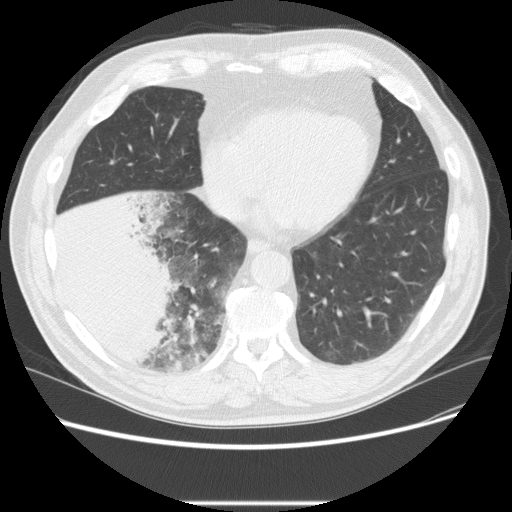
Low-dose screening chest CT, one axial slice. Position 73 of 233 along the scan axis. Reconstruction kernel STANDARD. Lung window (W 1500 / L -600 HU). 512 × 512 image matrix, field of view 380 × 380 mm.
Structures marked on this image (manually delineated by an expert):
- lesion 3 (tumor, lower lobe of right lung): bounding box (x1, y1, x2, y2) in pixels: (52, 192, 178, 368)